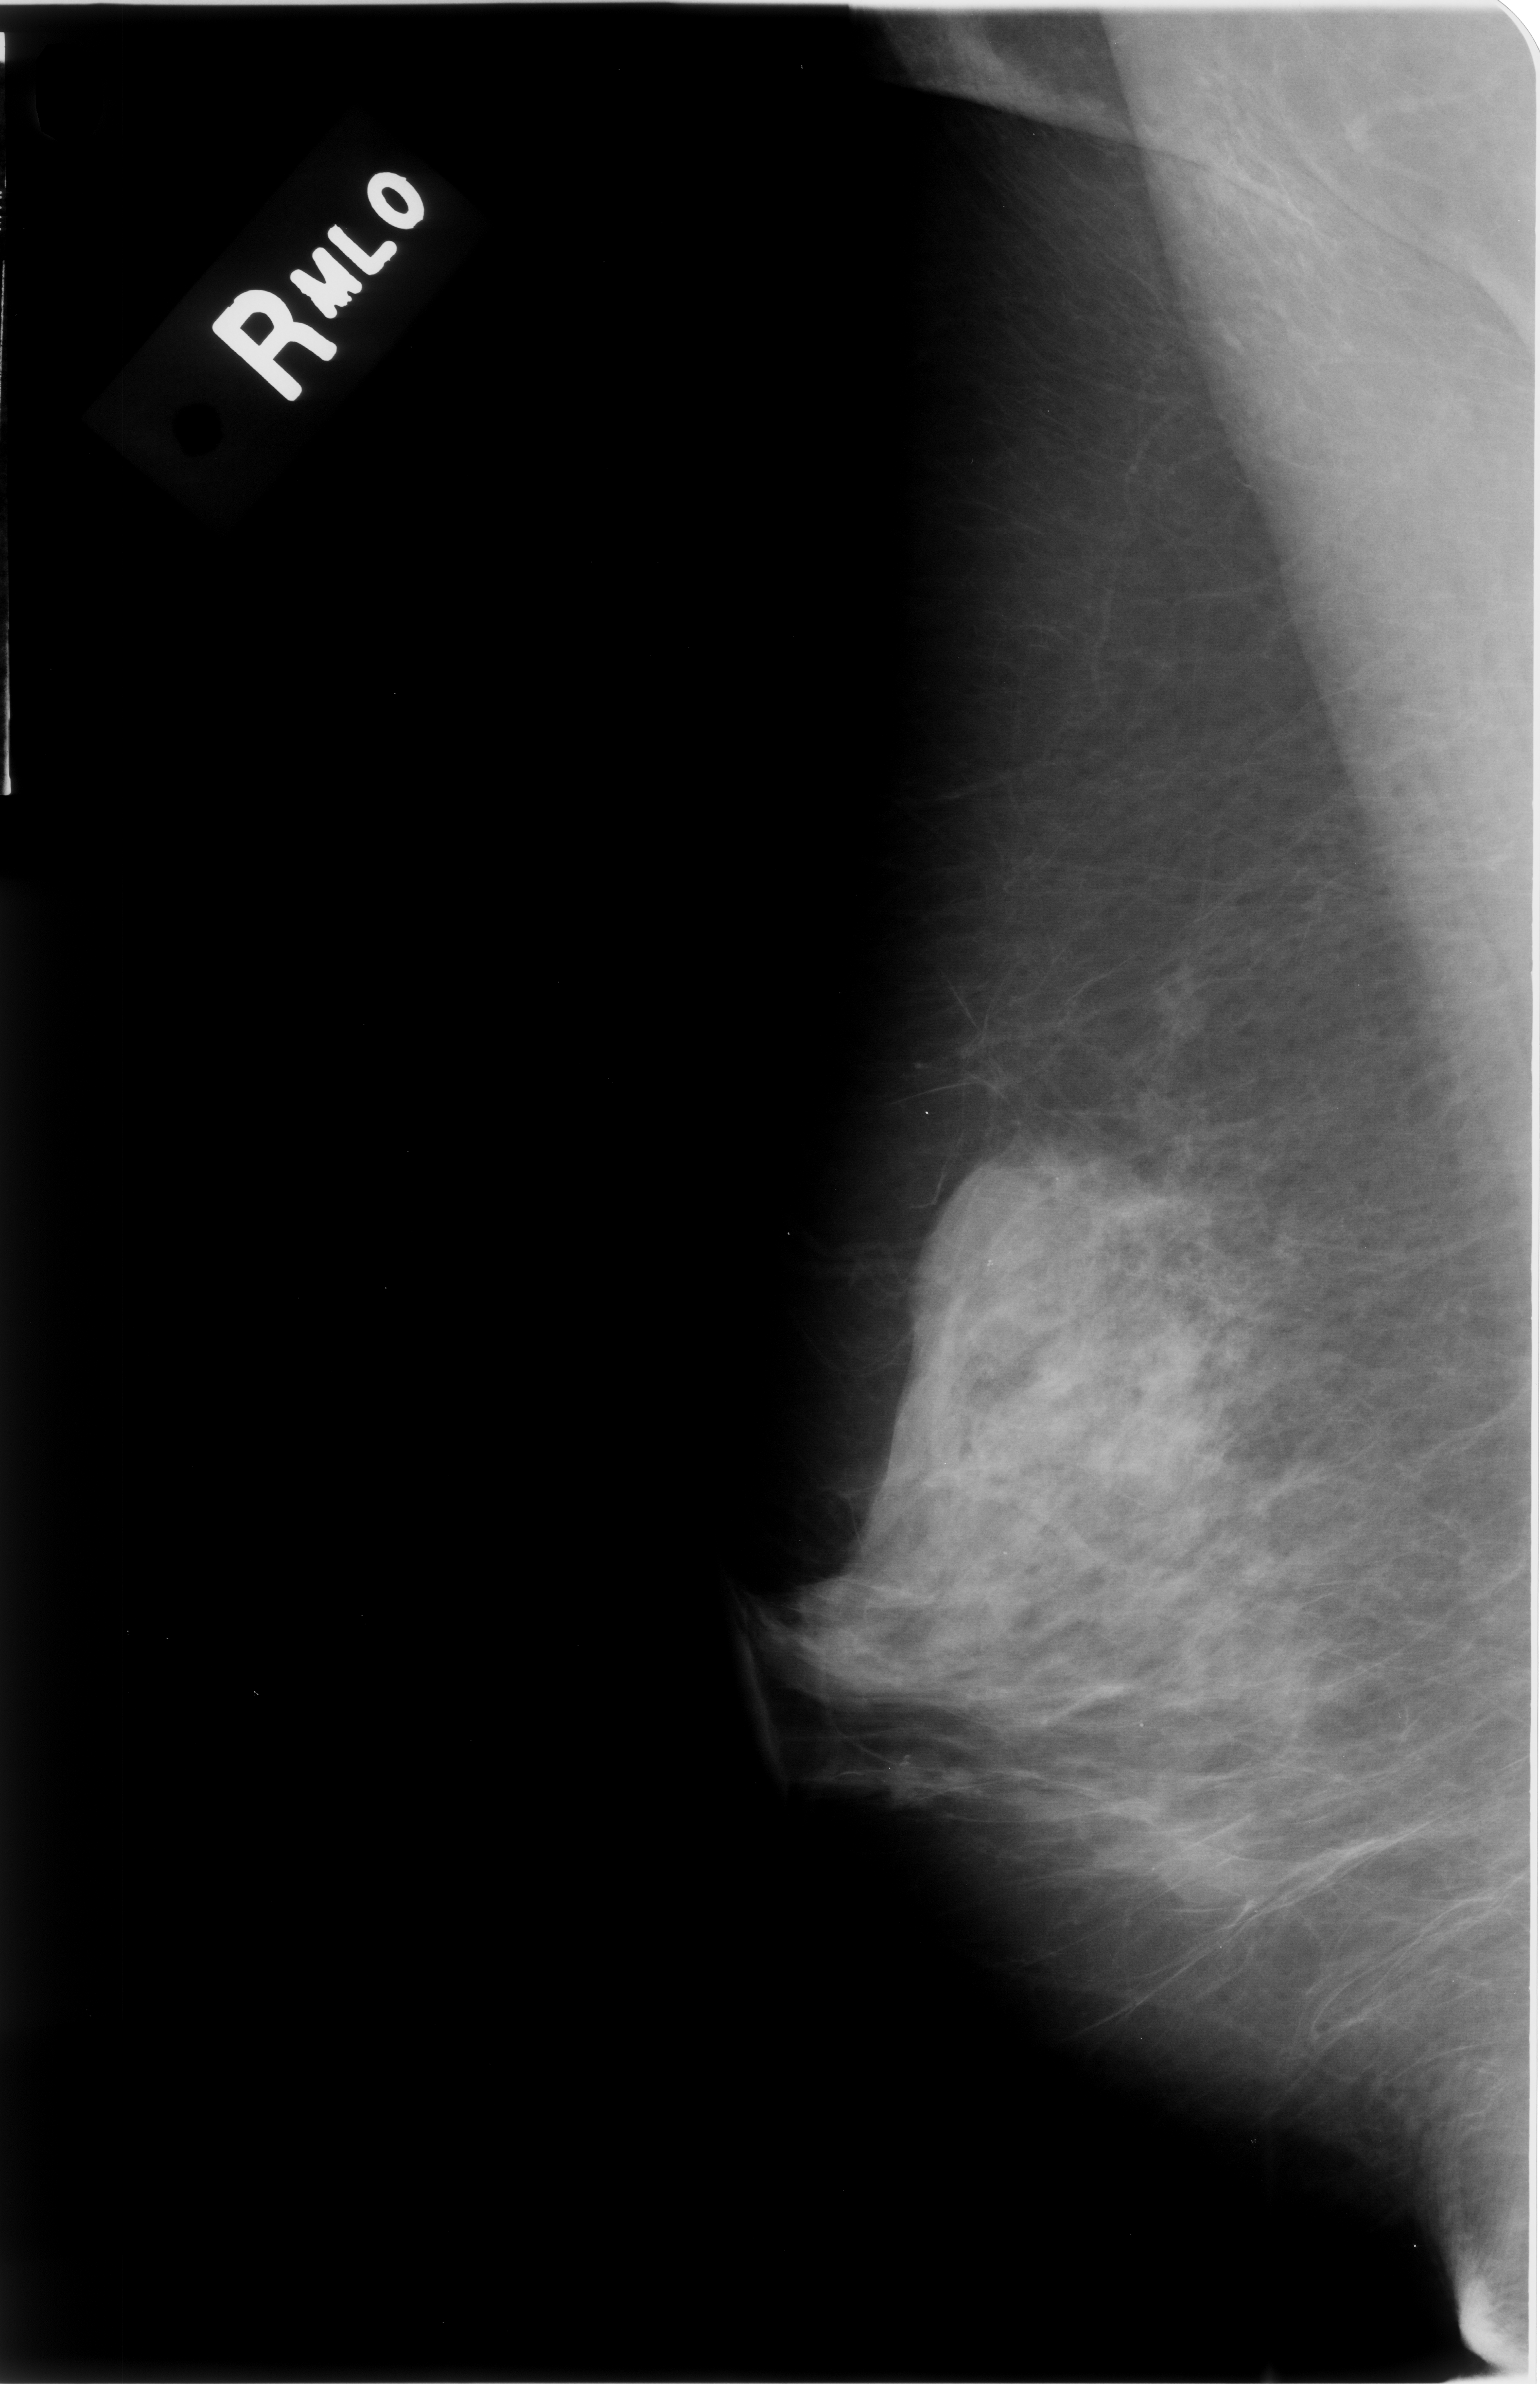
Mammogram (digitized film). Right breast. Mediolateral oblique (MLO) view. Breast composition: heterogeneously dense (BI-RADS density category 3 of 4). 1540 × 2384 image matrix.
Expert-marked regions of interest on this film, with their recorded descriptors:
- Finding 1 of 2: calcifications, morphology amorphous, distribution clustered; BI-RADS assessment category 4; subtlety rating 3 on a 1 (subtle) to 5 (obvious) scale; pathology (as recorded): benign: bounding box (x1, y1, x2, y2) in pixels: (860, 1712, 1002, 1883)
- Finding 2 of 2: calcifications, morphology amorphous, distribution clustered; BI-RADS assessment category 4; pathology result (as recorded, not read from the image): malignant: (934, 1148, 1072, 1331)